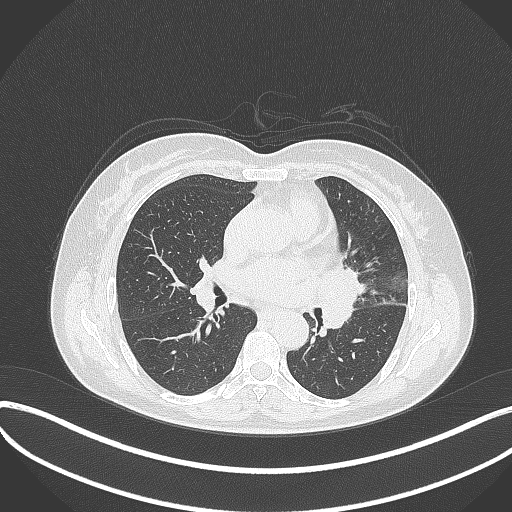
Chest CT, one axial slice. Position 184 of 373 along the scan axis. Reconstruction kernel B70f. 120 kVp. Lung window (W 1500 / L -600 HU). 1 mm slice thickness. 512 × 512 image matrix, field of view 400 × 400 mm. Patient: female, 54 years. Case-level facts recorded for this patient, not image findings: clinical TNM (as recorded): T2a N1 M0; histopathological grade: G3.
Structures marked on this image (rectangle marked by the reading radiologist):
- lung tumour (recorded histology: small cell carcinoma): box from (x=317, y=268) to (x=365, y=335) px